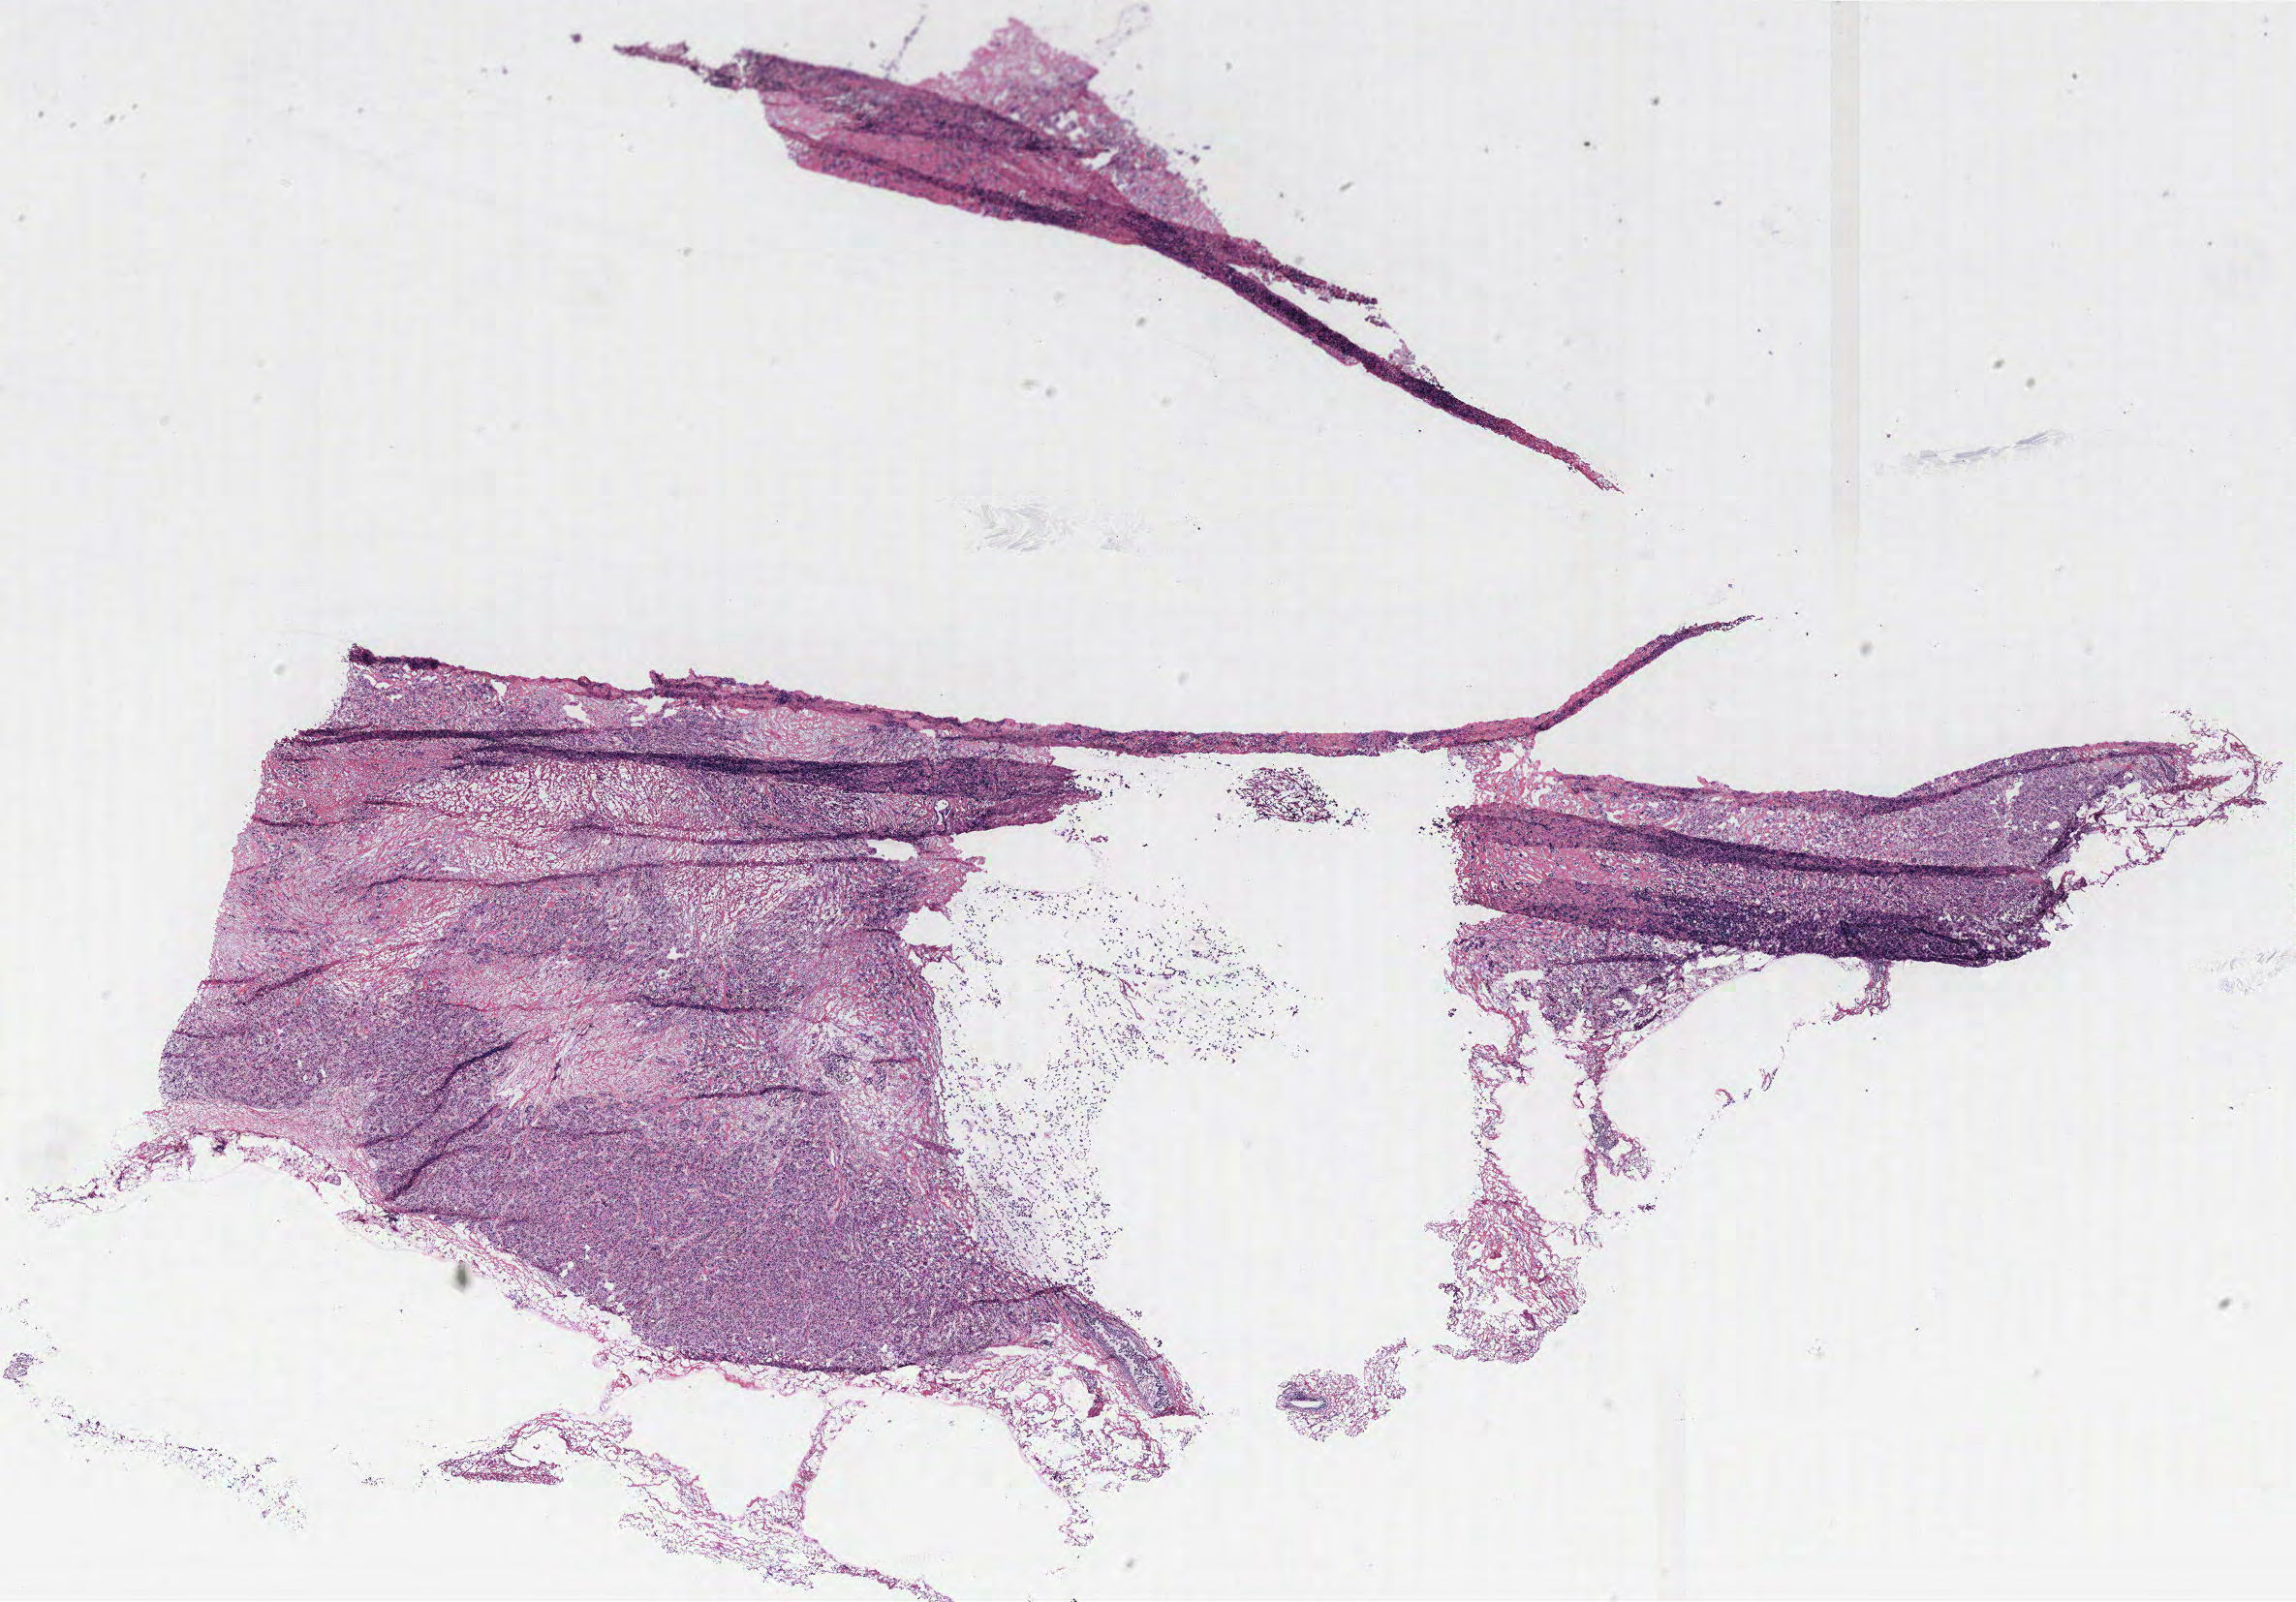
Whole-slide histology image, H&E-stained, low-resolution overview of the scanned area, about 19.0 x 13.2 mm, breast, tissue type not recorded. Female, 61 y/o.
- patient diagnosis: Infiltrating duct carcinoma, NOS